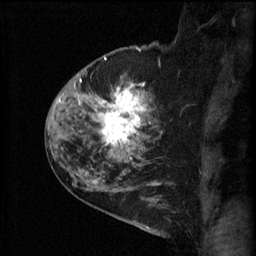
Breast MRI (dynamic contrast-enhanced), one sagittal slice. Position 43 of 60 along the scan axis. 3 images stored at this slice position (order not interpretable as contrast timing). 1.5 T. TE 4.2 ms, TR 11 ms. 256 × 256 image matrix, field of view 180 × 180 mm. Patient: female, 52 years.
Outlined on this slice (semi-automatic segmentation, software-assisted and operator-edited):
- analysis volume of interest (the breast-tissue region the enhancement analysis was run in; not a lesion): box from (x=86, y=76) to (x=165, y=157) px
- tumour enhancement mask (voxels above the 70 % enhancement threshold inside the analysis volume of interest): (x=89, y=84)–(x=145, y=155)